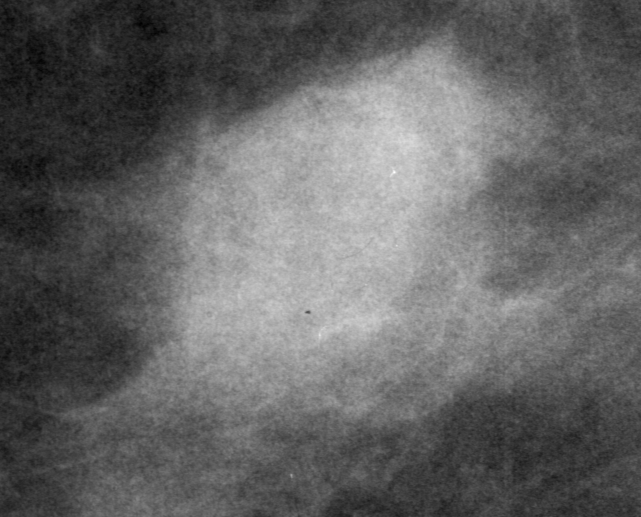
Crop from a digitized film mammogram around one marked abnormality; left breast; CC view.
Marked abnormality: mass, shape oval, margins microlobulated; BI-RADS assessment category 0 (incomplete: needs additional imaging); subtlety rating 5 on a 1 (subtle) to 5 (obvious) scale; pathology result (as recorded, not read from the image): benign.